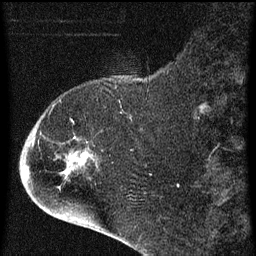
Breast MRI (dynamic contrast-enhanced), one sagittal slice. Position 19 of 60 along the scan axis. Dynamic contrast-enhanced series, image 2 of 4 at this slice position (ordered by acquisition). 1.5 T. TE 4.2 ms, TR 8 ms. 256 × 256 image matrix, field of view 180 × 180 mm. Female patient, age 71 years.
Outlined on this slice (semi-automatically segmented with operator editing):
- analysis volume of interest (the breast-tissue region the enhancement analysis was run in; not a lesion): bounding box [x1, y1, x2, y2] px = [32, 90, 135, 205]
- tumour enhancement mask (voxels above the 70 % enhancement threshold inside the analysis volume of interest): [68, 154, 87, 165]